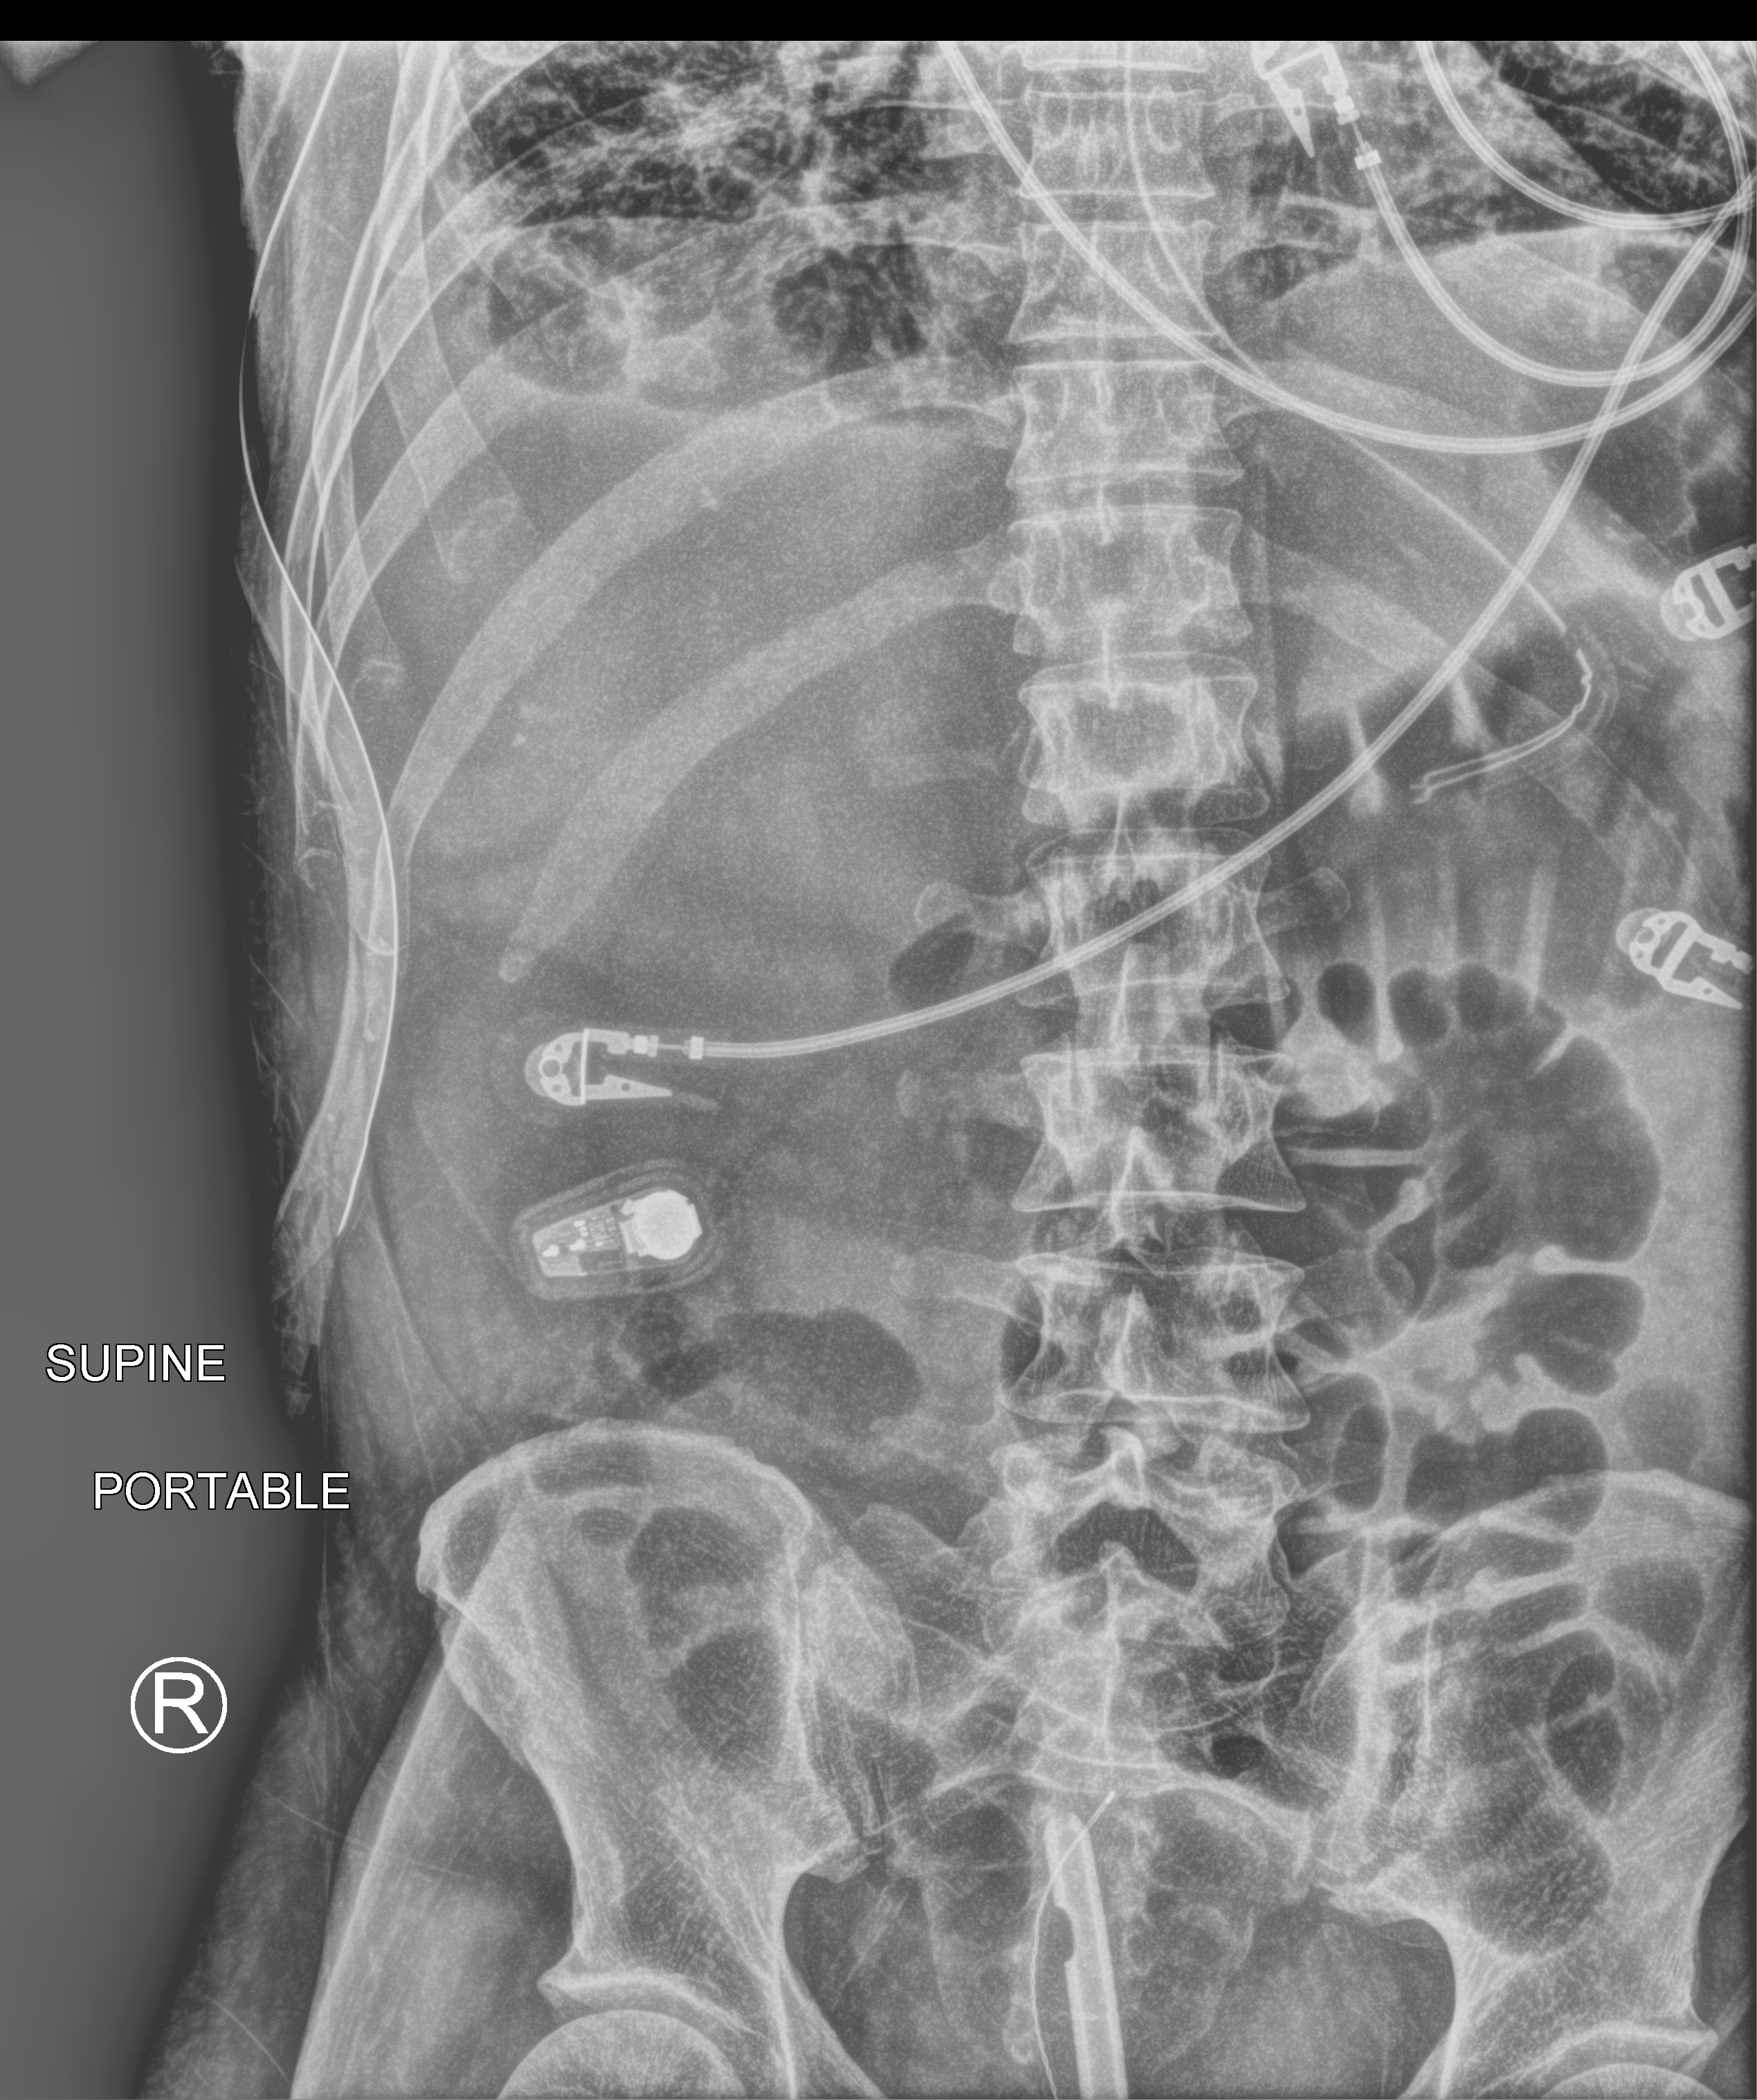
Abdomen radiograph, anteroposterior (AP) projection. Patient hospitalised with COVID-19; male, aged 18–59 years.
From the hospital-stay record, not from the radiograph (when in the stay this image was taken is not recorded):
- mechanically ventilated during this hospital stay: yes
- COPD (admission record): no